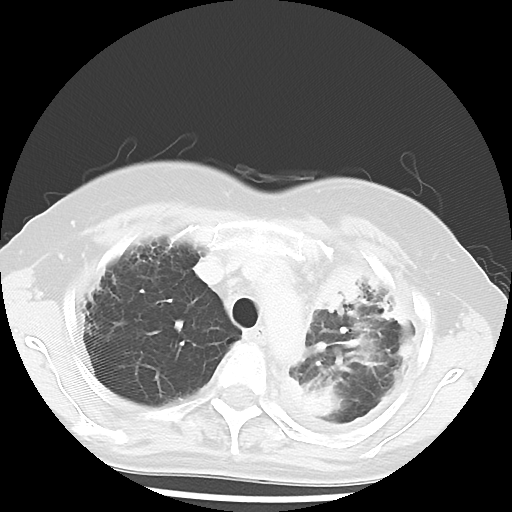
Chest CT, one axial slice. Position 43 of 56 along the scan axis. Lung window (W 1500 / L -600 HU). 5 mm slice thickness. 512 × 512 image matrix, field of view 309 × 309 mm. Female patient, age 56 years. From the clinical record (not read from this slice): clinical TNM (as recorded): T1c N0 M1.
Outlined on this slice (bounding box drawn by a radiologist):
- lung tumour (recorded histology: adenocarcinoma): bounding box (x1, y1, x2, y2) in pixels: (313, 257, 366, 324)